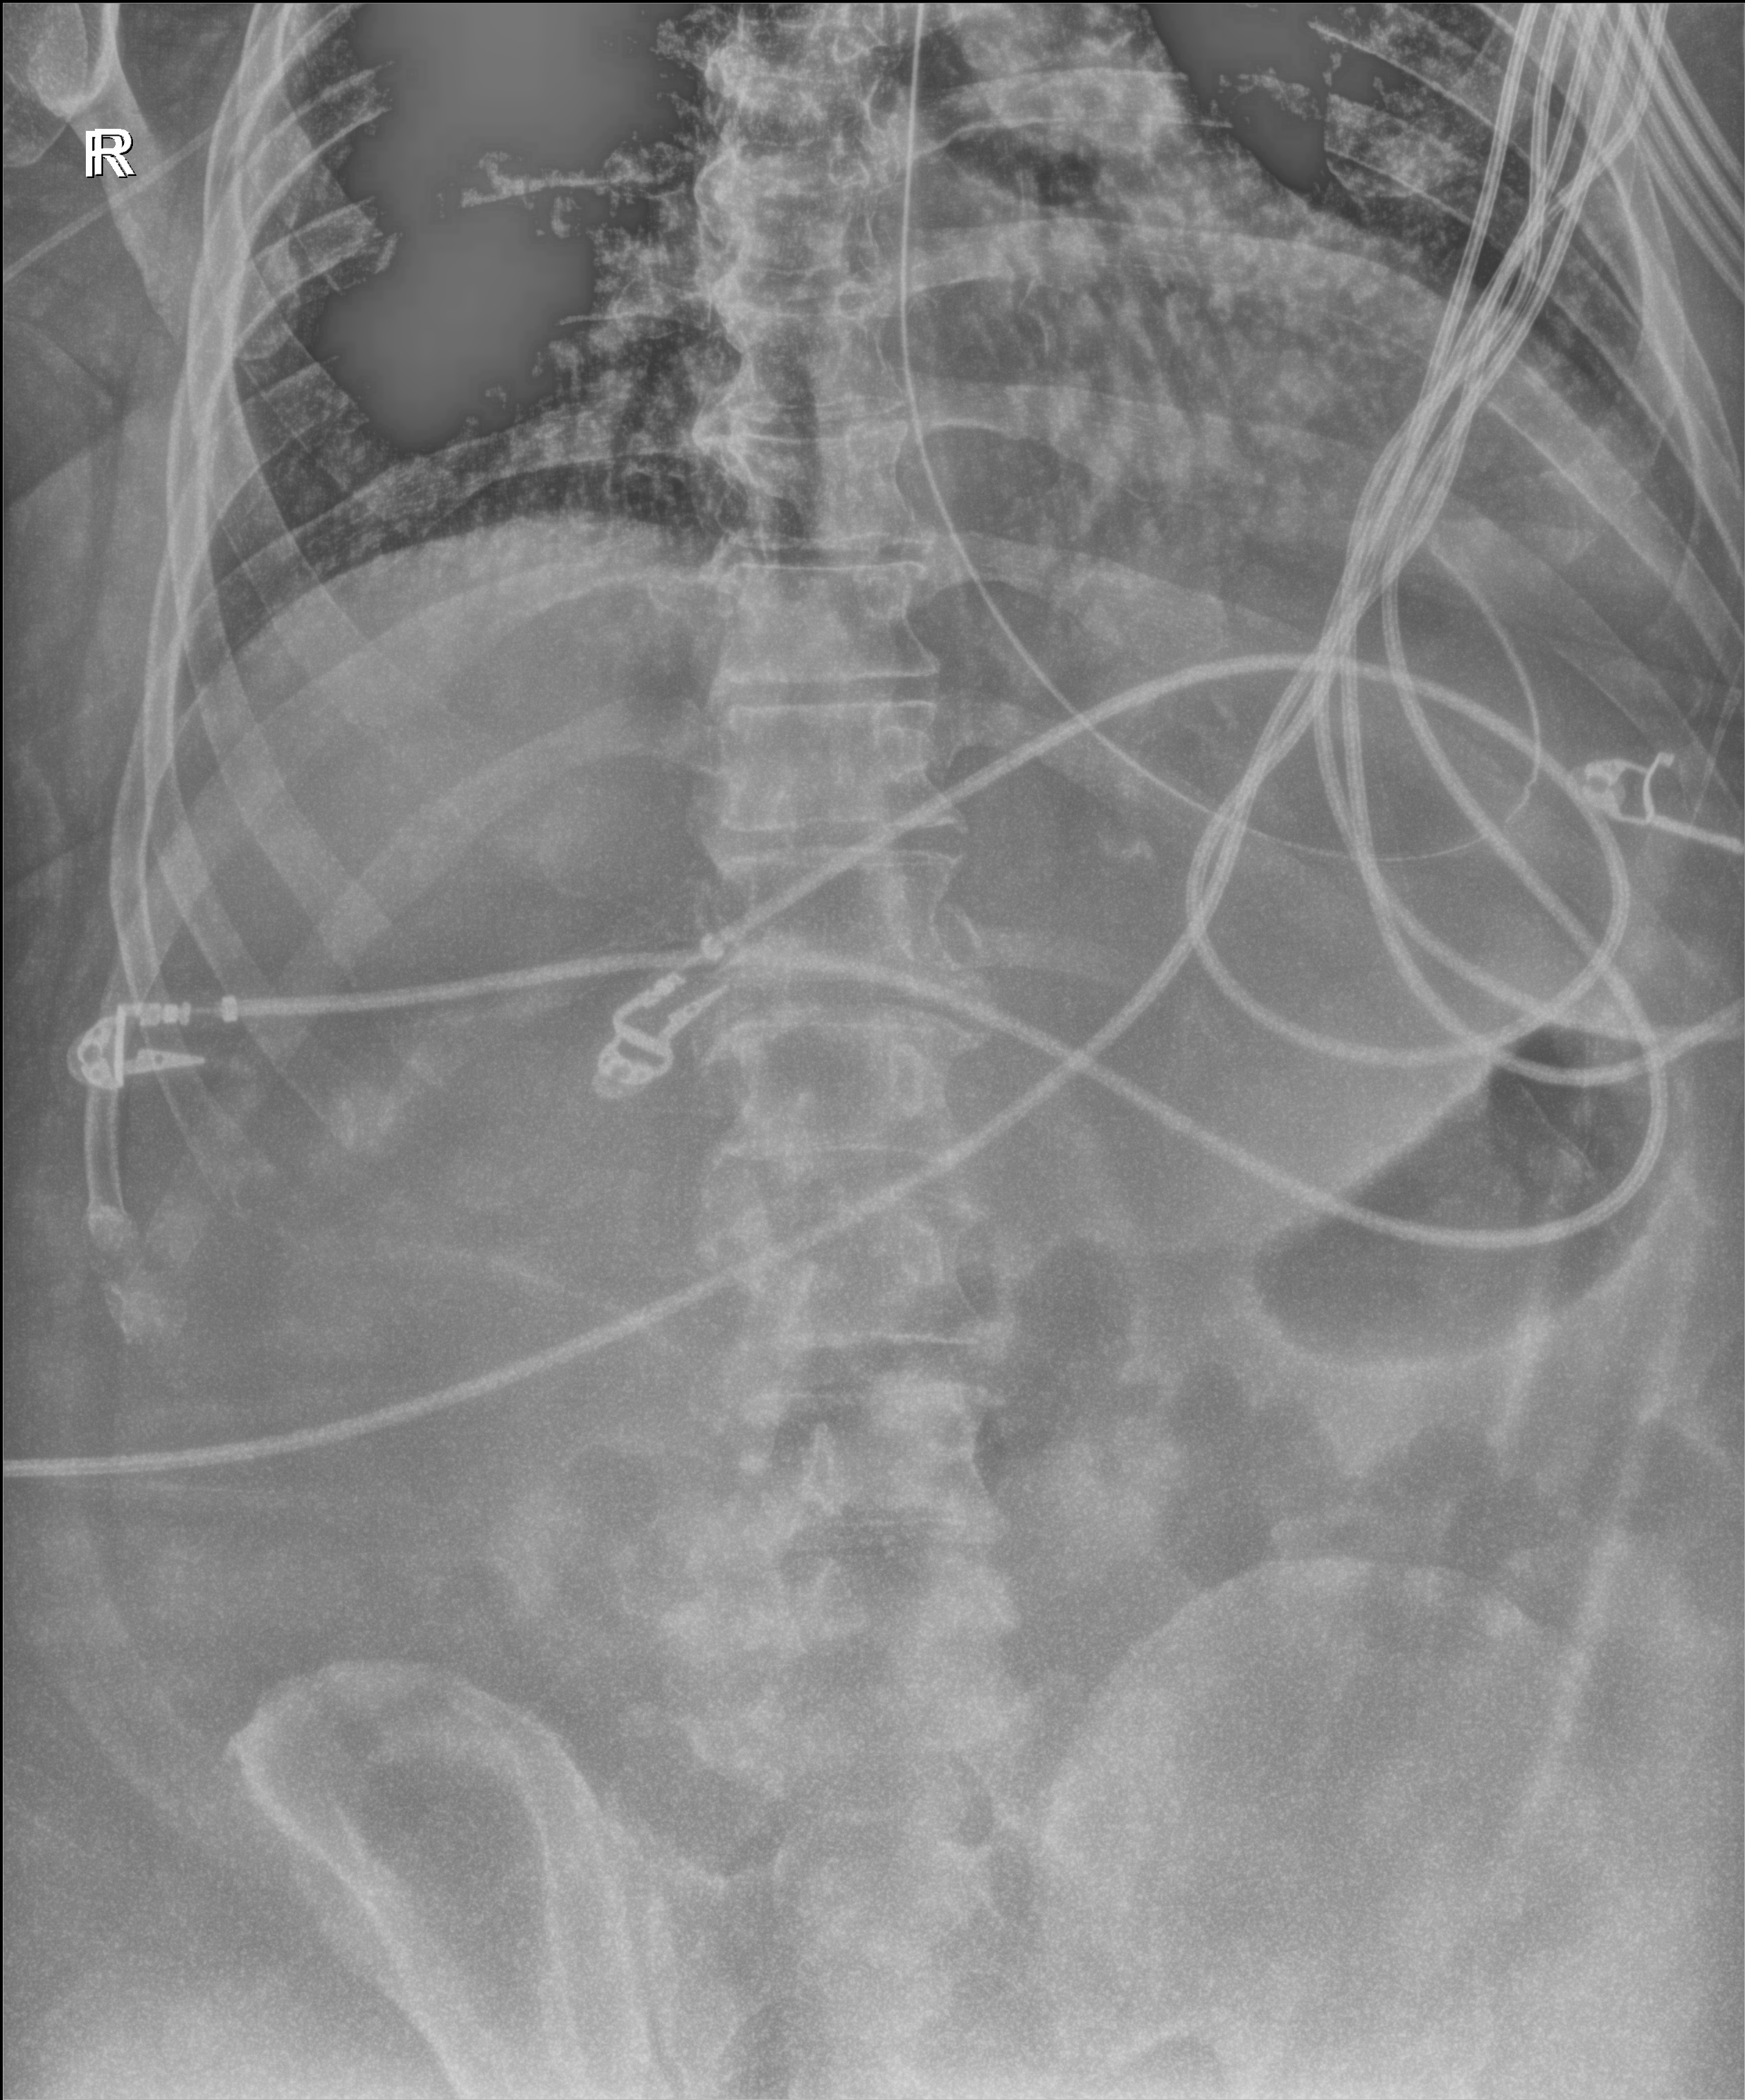
Abdomen X-ray (portable); anteroposterior (AP) projection. Patient hospitalised with COVID-19, aged 18–59 years.
From the hospital-stay record, not from the radiograph (when in the stay this image was taken is not recorded):
- admitted to intensive care during this hospital stay: yes